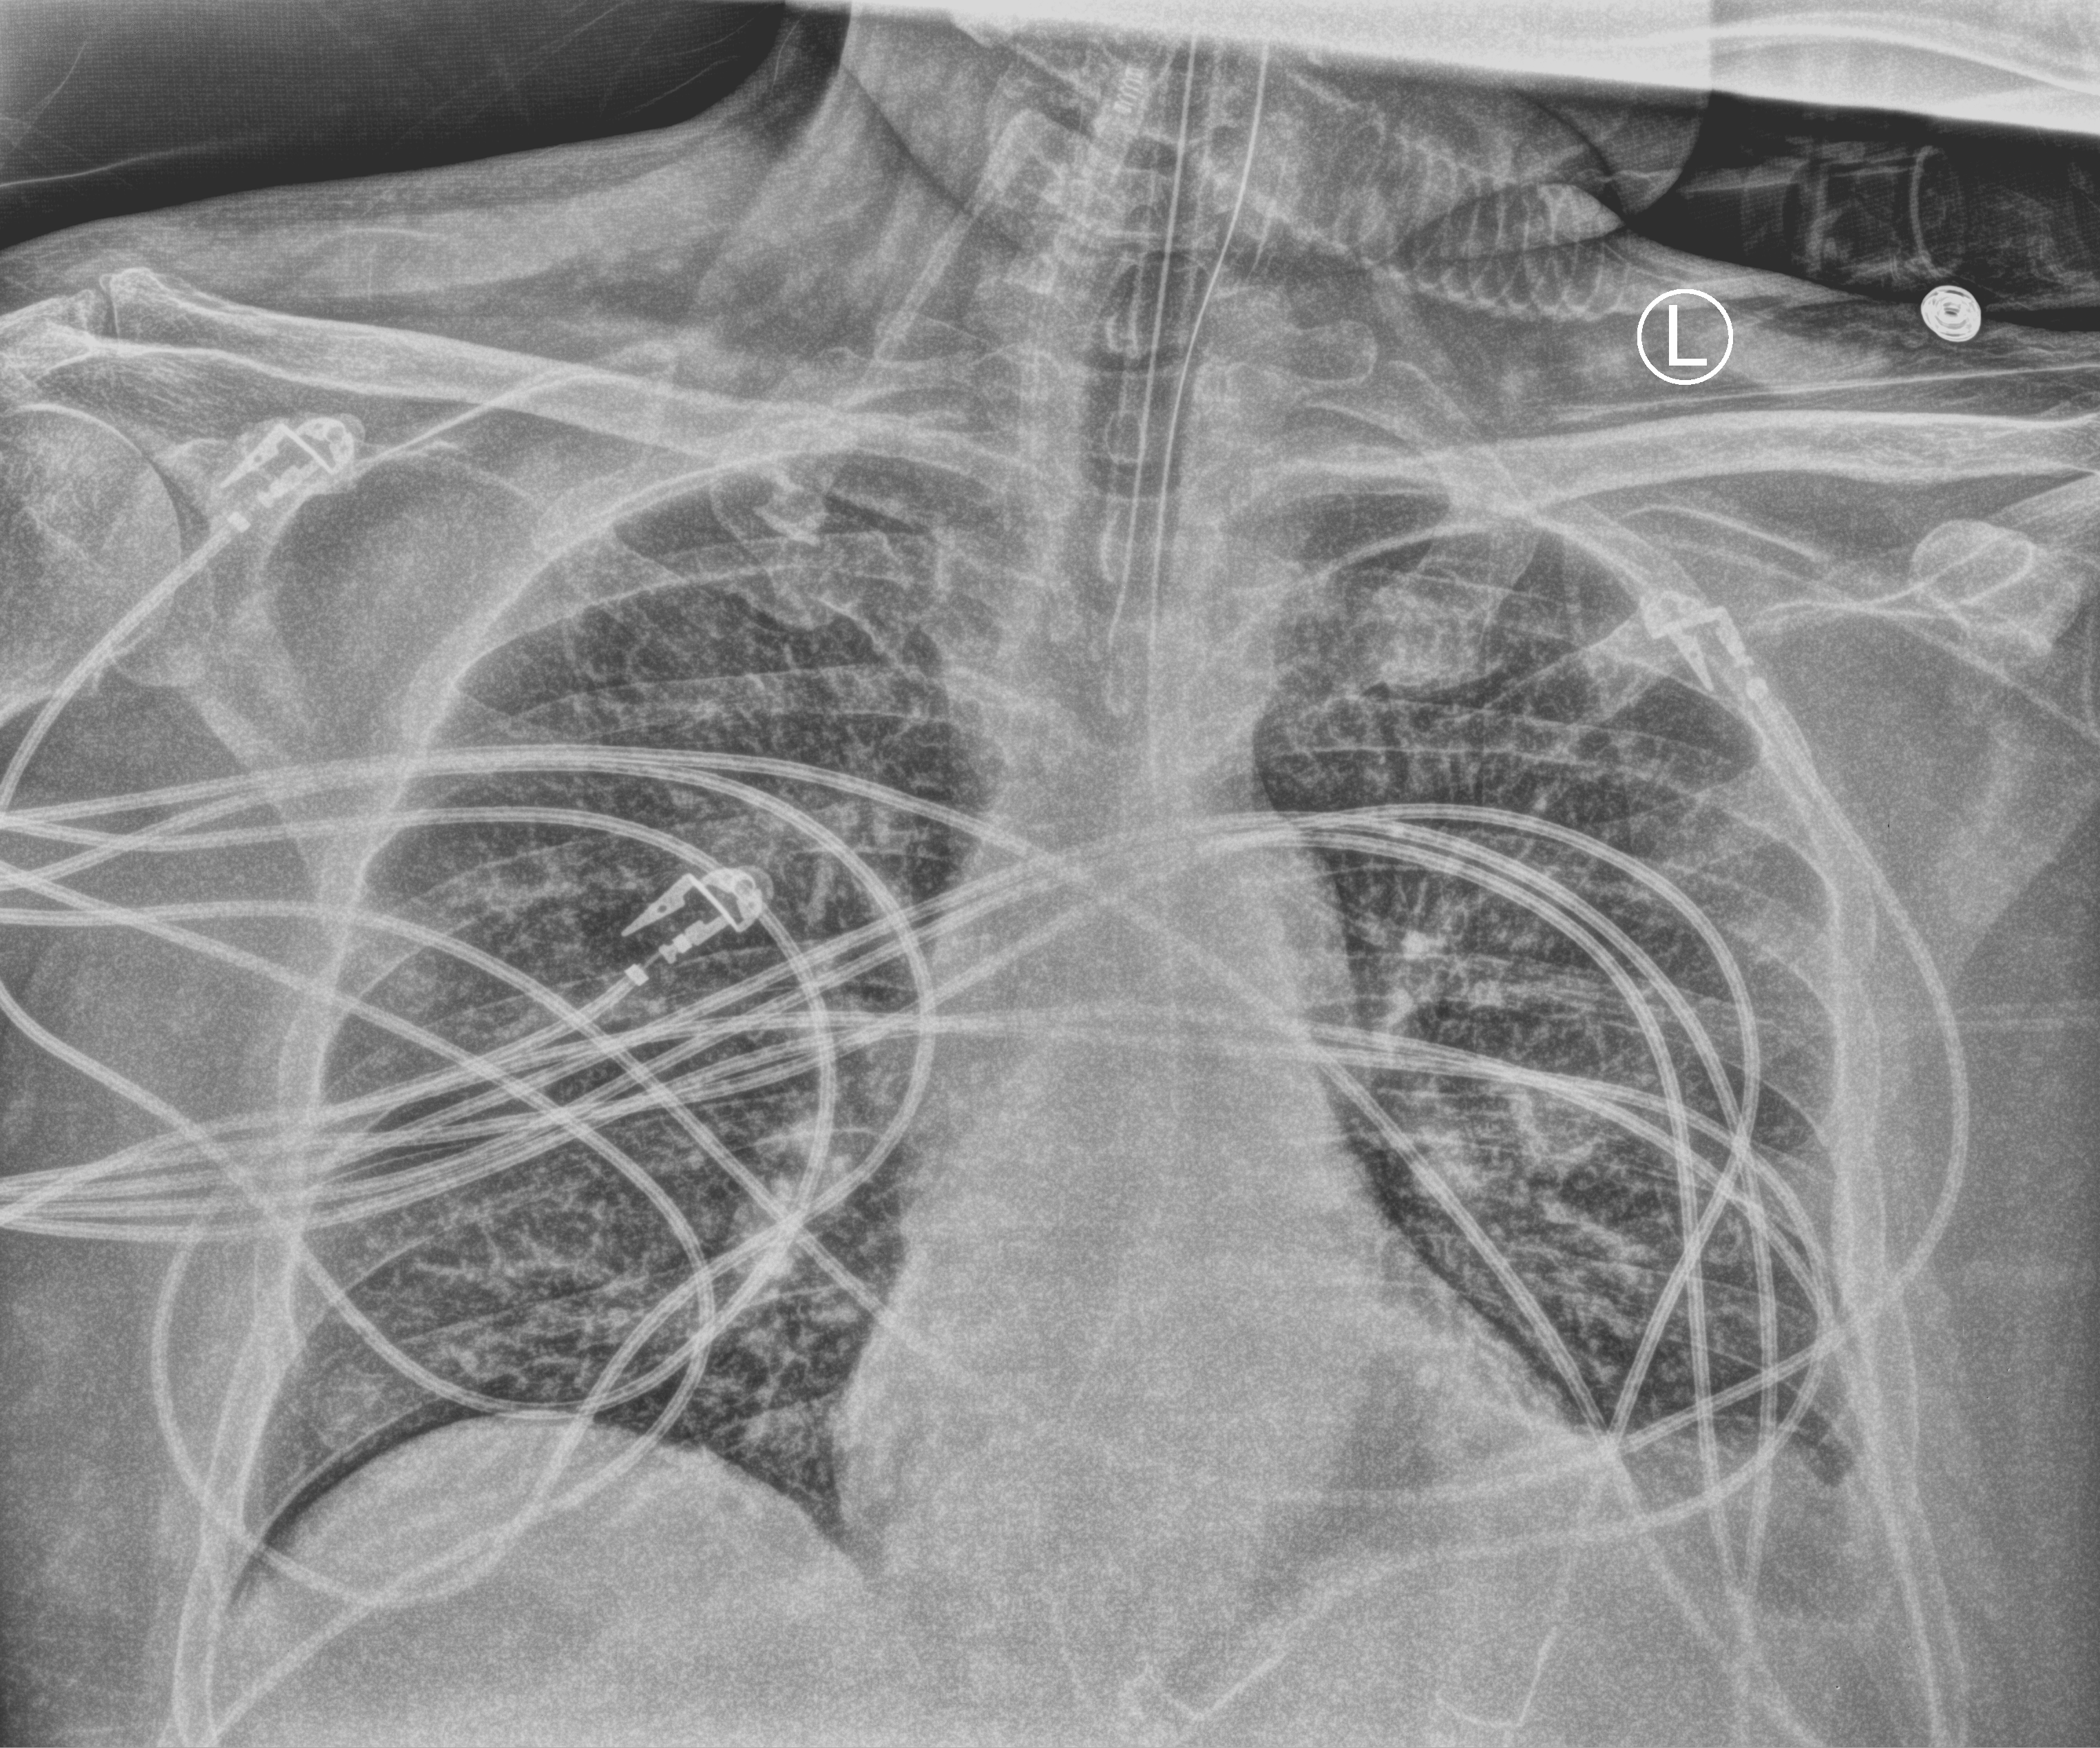
Portable chest radiograph; anteroposterior (AP) projection. Male patient hospitalised with COVID-19, age 60–74 years.
From the hospital-stay record, not from the radiograph (when in the stay this image was taken is not recorded): diabetes (admission record): no.